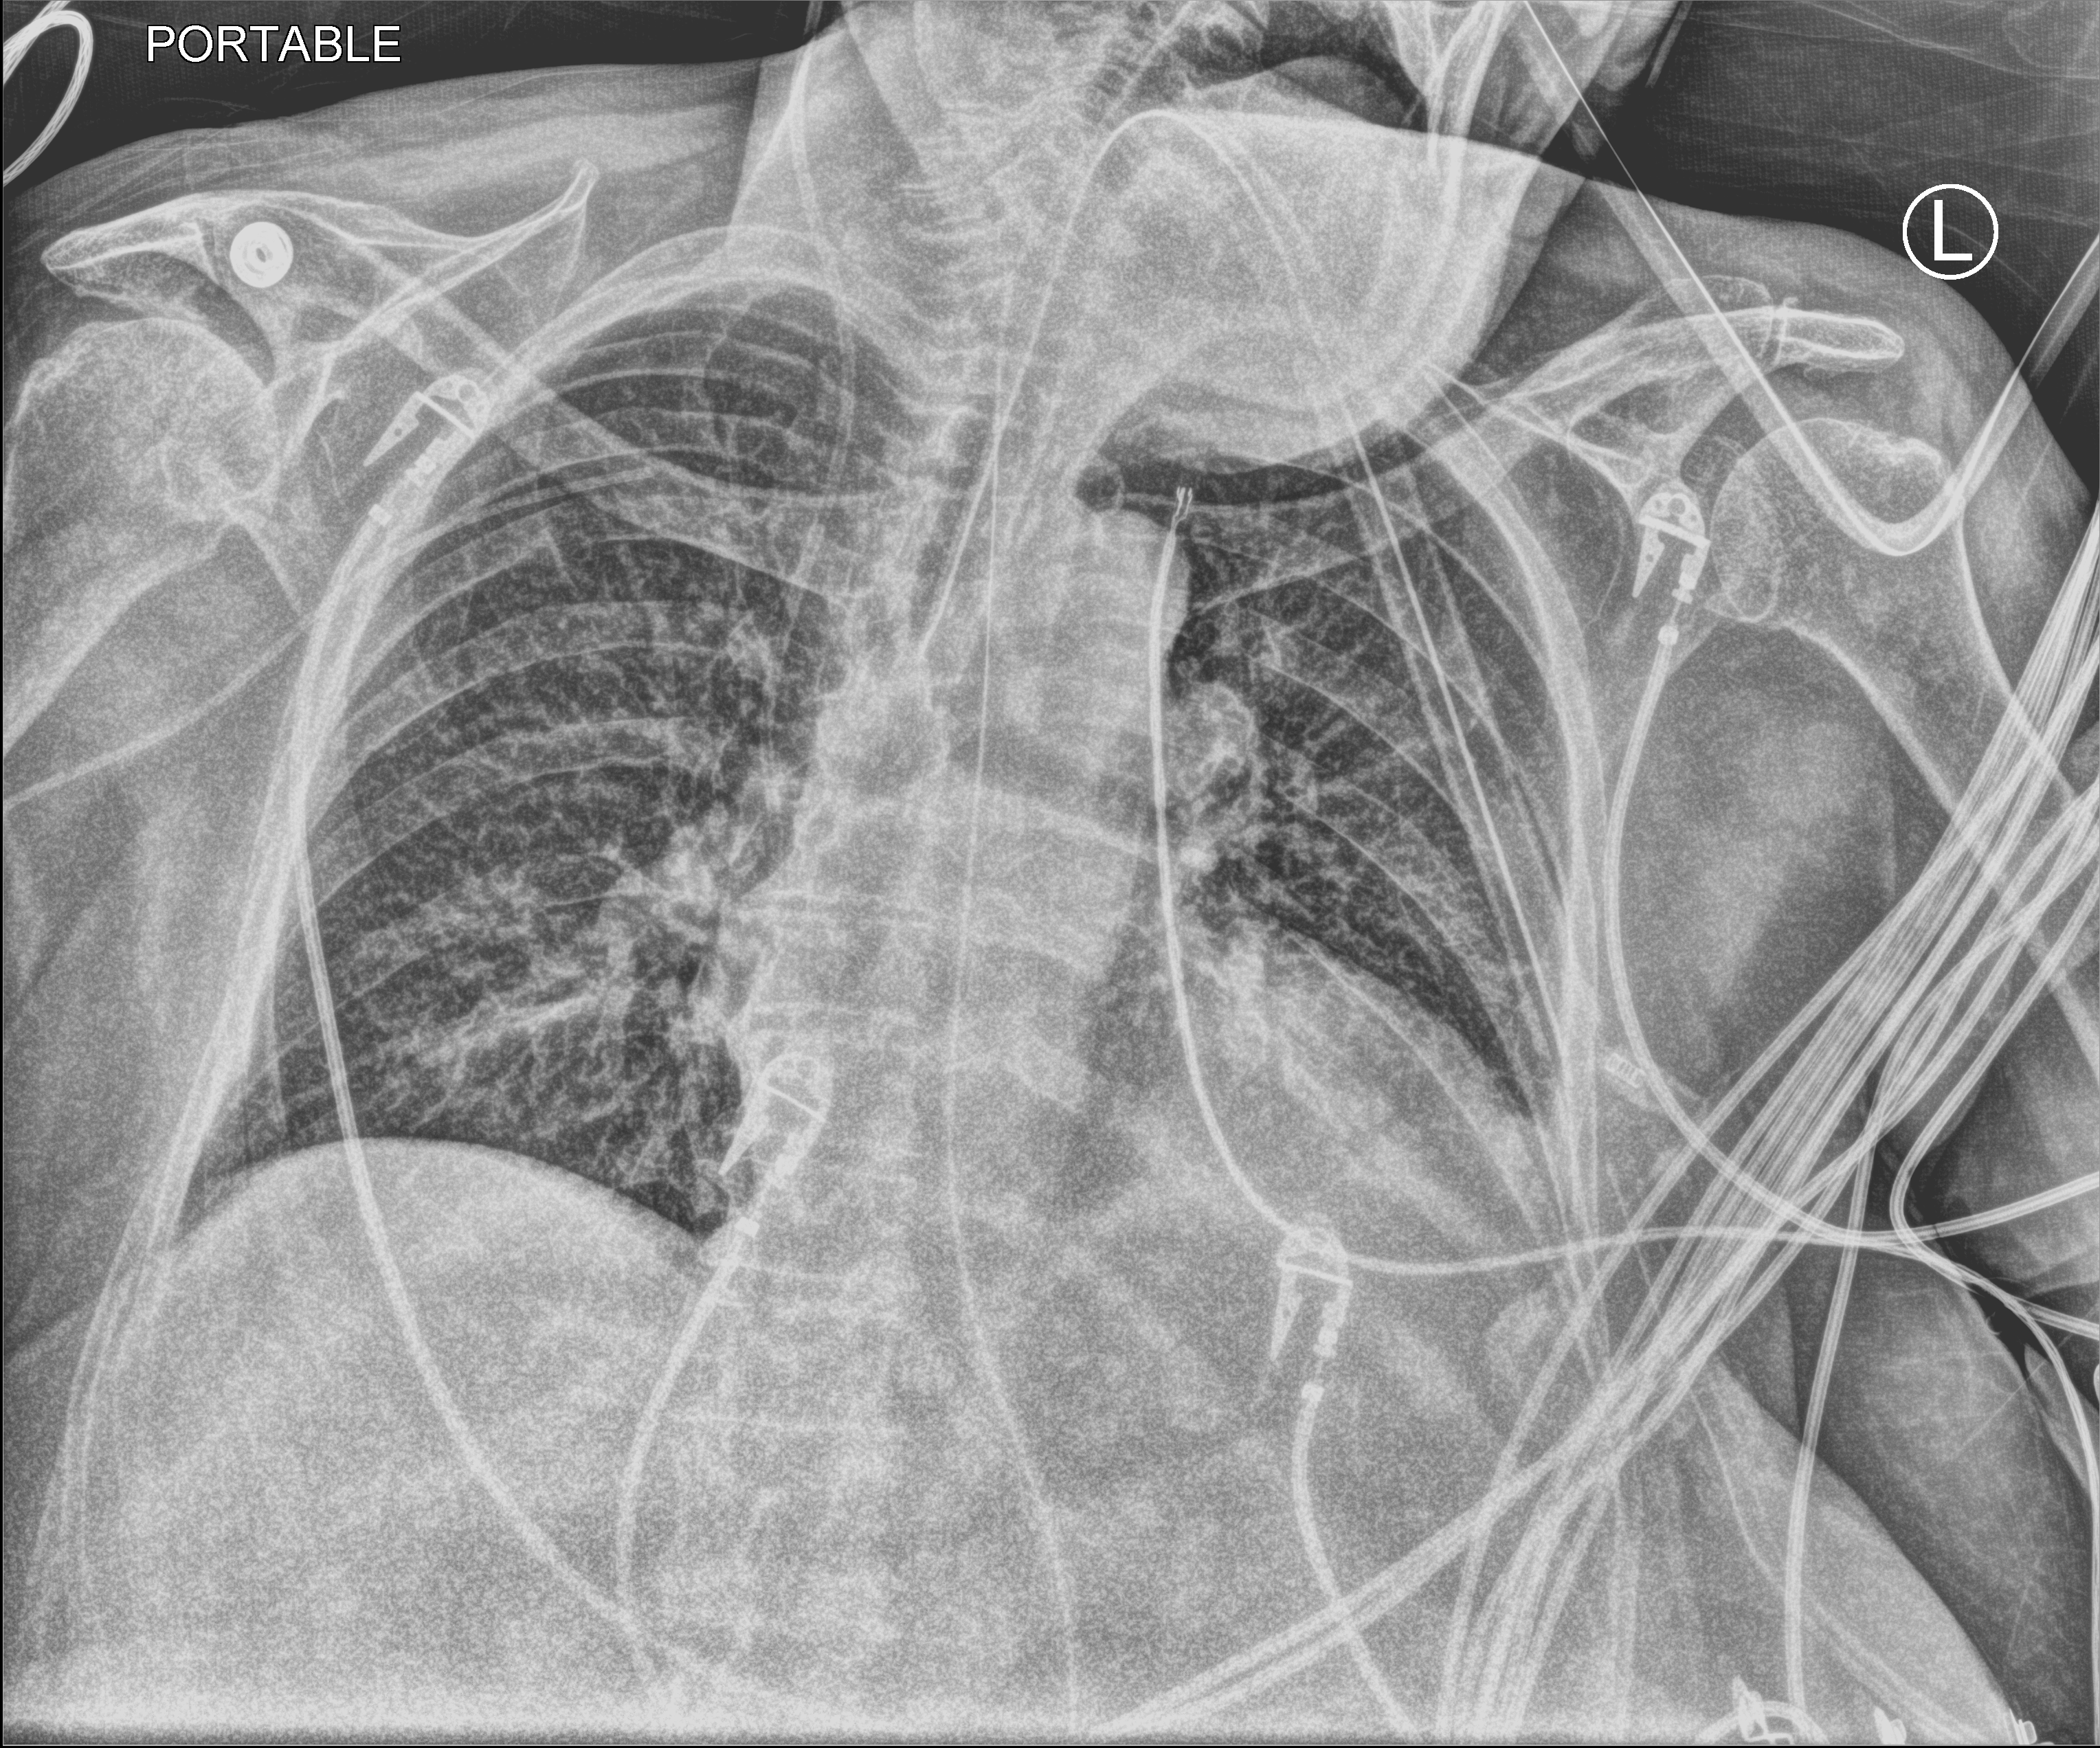
Bedside chest radiograph (computed radiography); anteroposterior (AP) projection. Female patient hospitalised with COVID-19, age 75–90 years.
Admission-level facts for this patient (not findings on this image; timing relative to this image not recorded): smoking status (admission record): never; other chronic lung disease (admission record): no; chronic kidney disease (admission record): no.